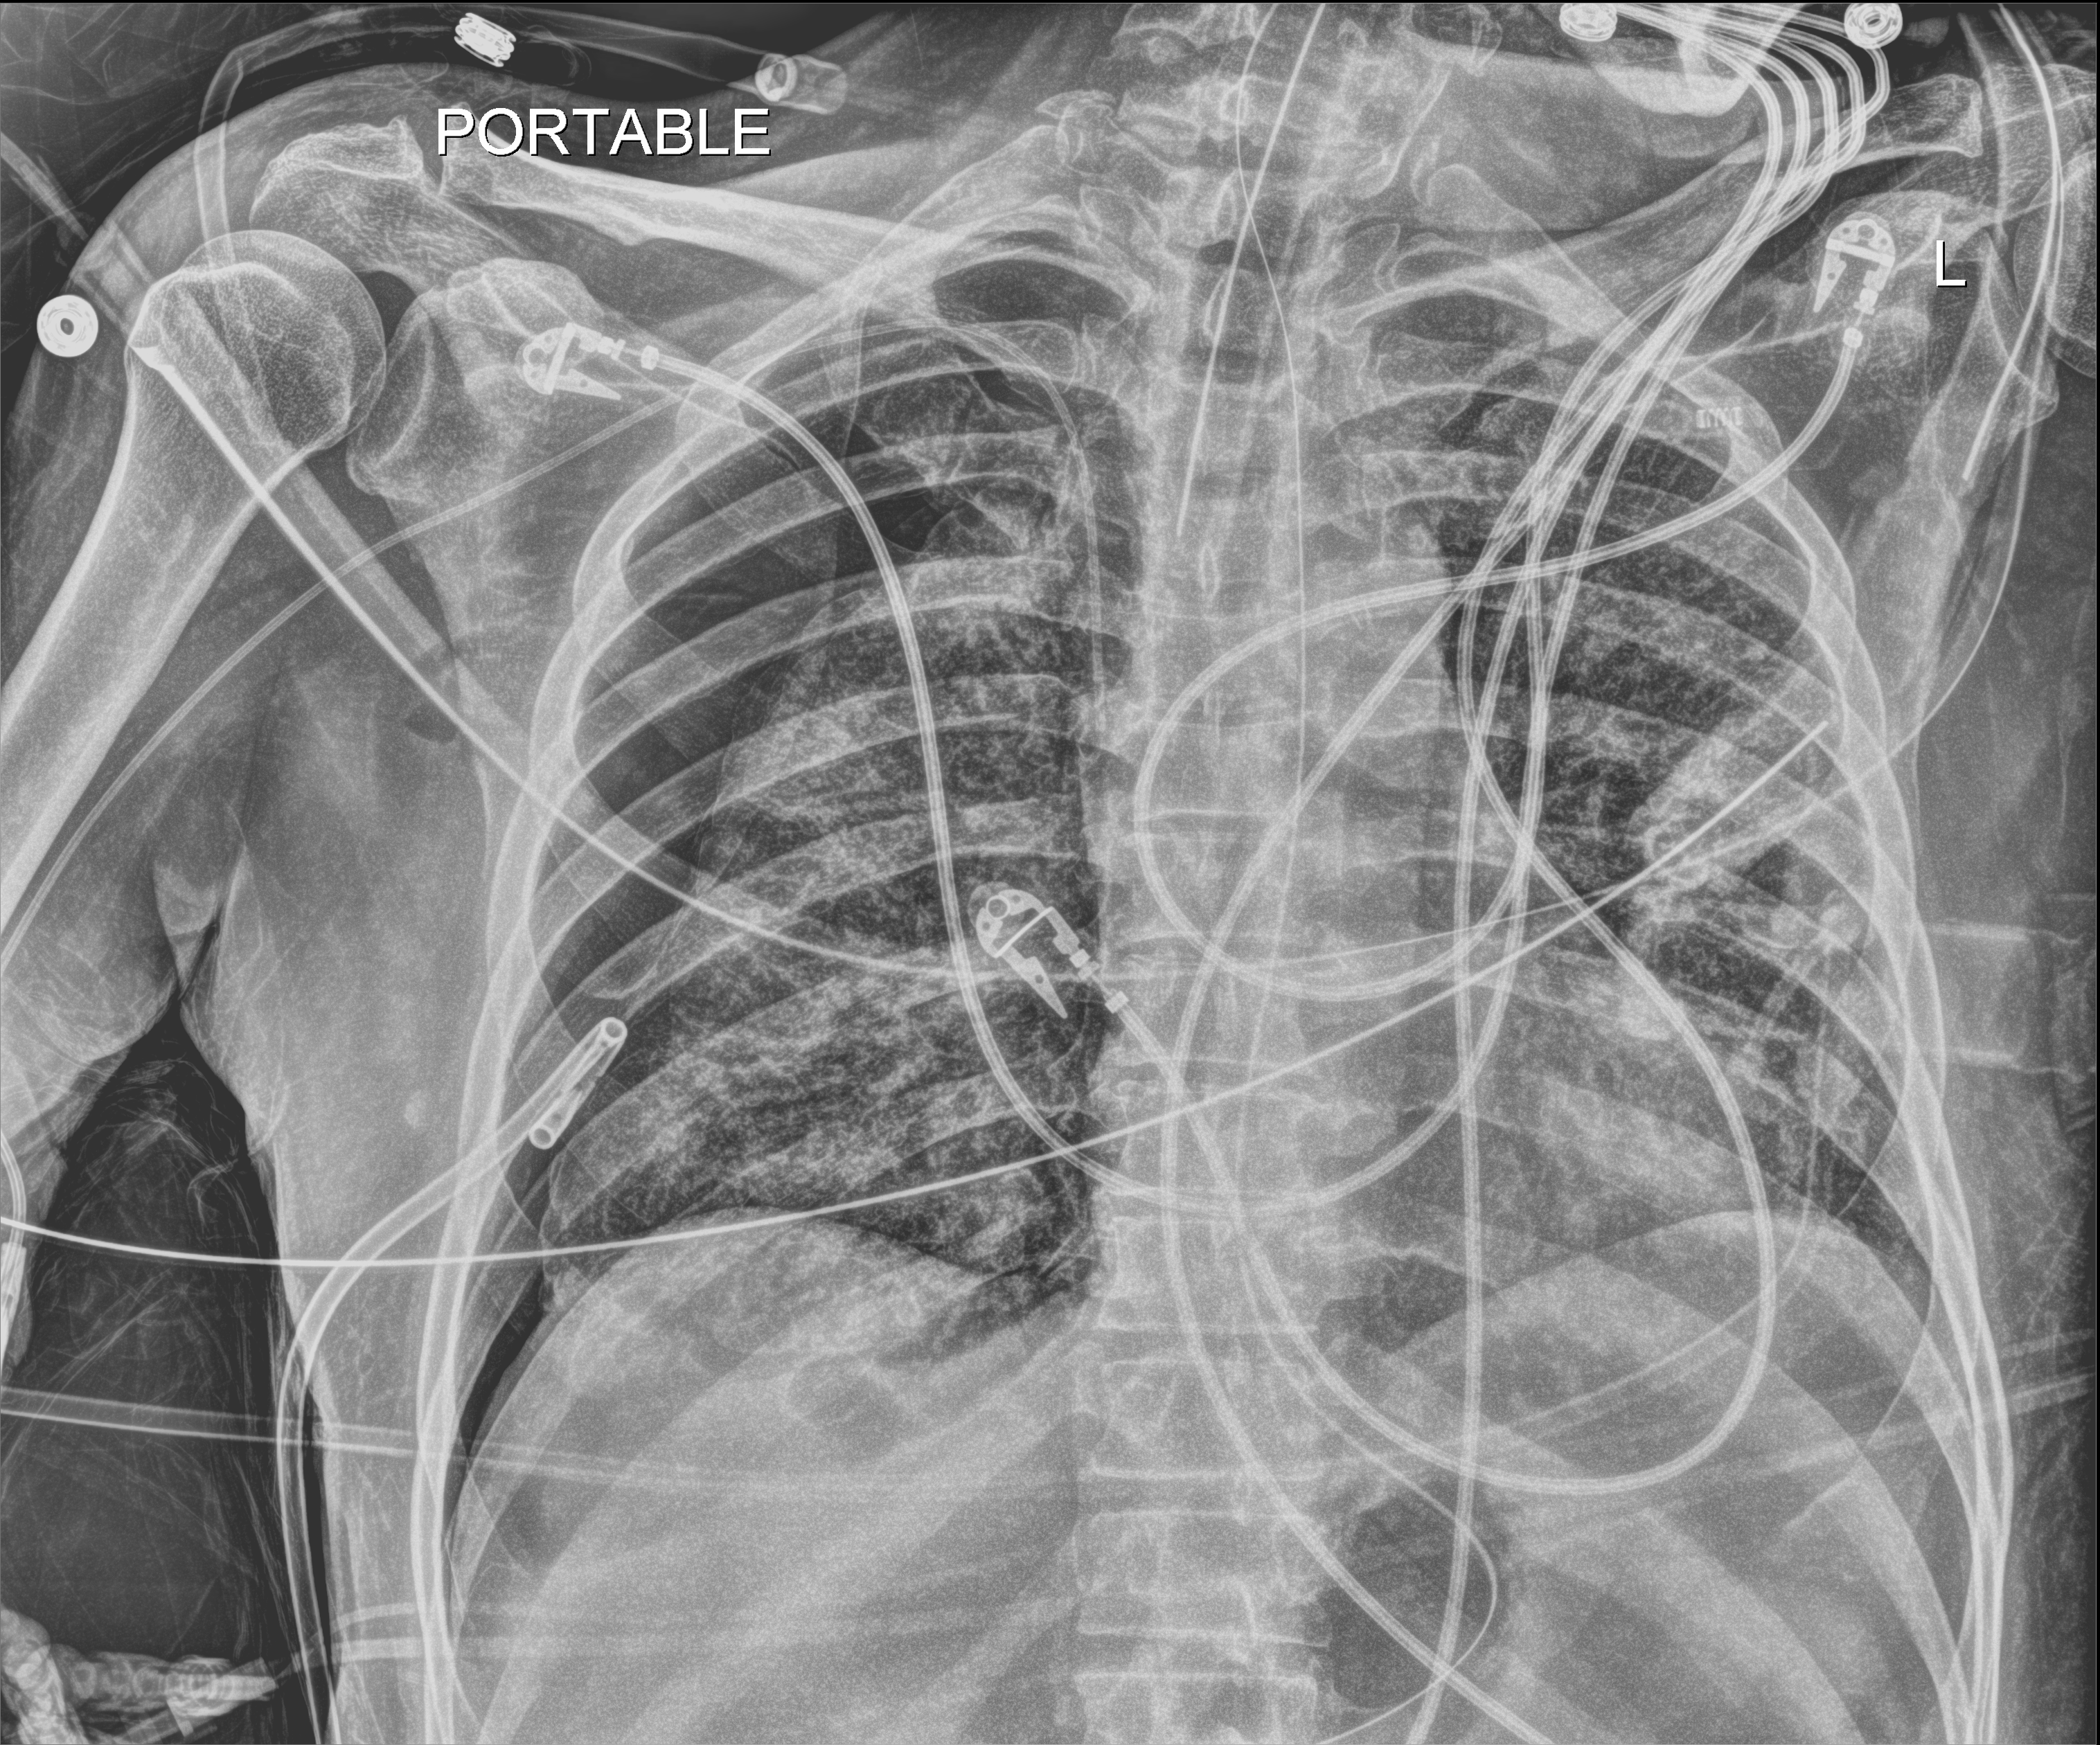
Portable chest radiograph, anteroposterior (AP) projection. Male patient hospitalised with COVID-19, age 18–59 years.
From the hospital-stay record, not from the radiograph (when in the stay this image was taken is not recorded): mechanically ventilated during this hospital stay: yes; admitted to intensive care during this hospital stay: yes.